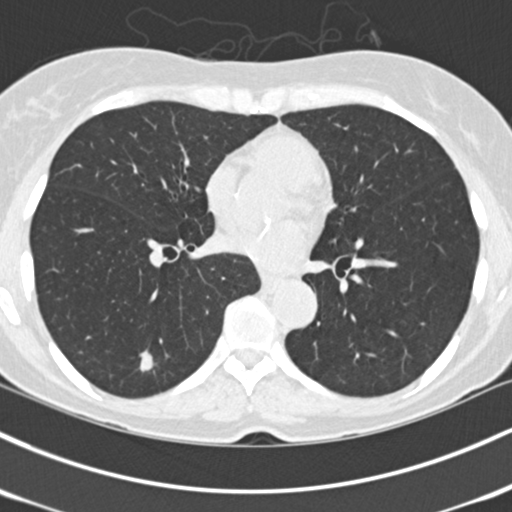
Low-dose screening chest CT, one axial slice; slice 65 of 150 in the series (ordered by position); 120 kVp; lung window (W 1500 / L -600 HU); 2 mm slice thickness; 512 × 512 image matrix, field of view 318 × 318 mm.
Structures marked on this image (outlined manually by an expert reader):
- lesion 1 (tumor): box from (x=140, y=350) to (x=153, y=372) px